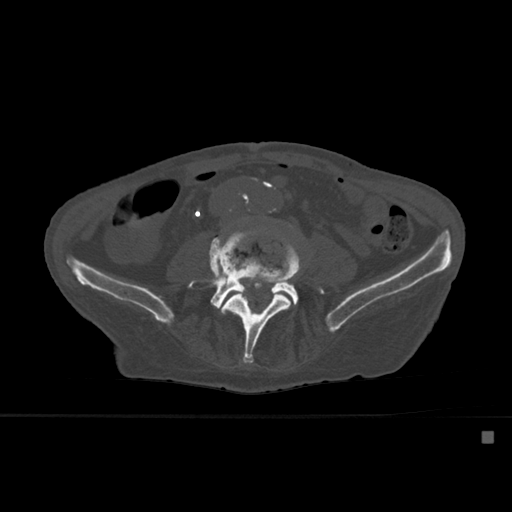
CT including the spine, one axial slice; slice 187 of 527 in the series (ordered by position); bone window (W 1800 / L 400 HU); 1.5 mm slice thickness; 512 × 512 image matrix. Patient: male, 78 years. From the clinical record (not read from this slice): primary cancer: prostate.
Annotated regions visible in this slice (semi-automatically segmented with operator editing):
- L4 vertebra: bounding box [x1, y1, x2, y2] px = [221, 240, 302, 363]
- L5 vertebra: [190, 227, 323, 314]